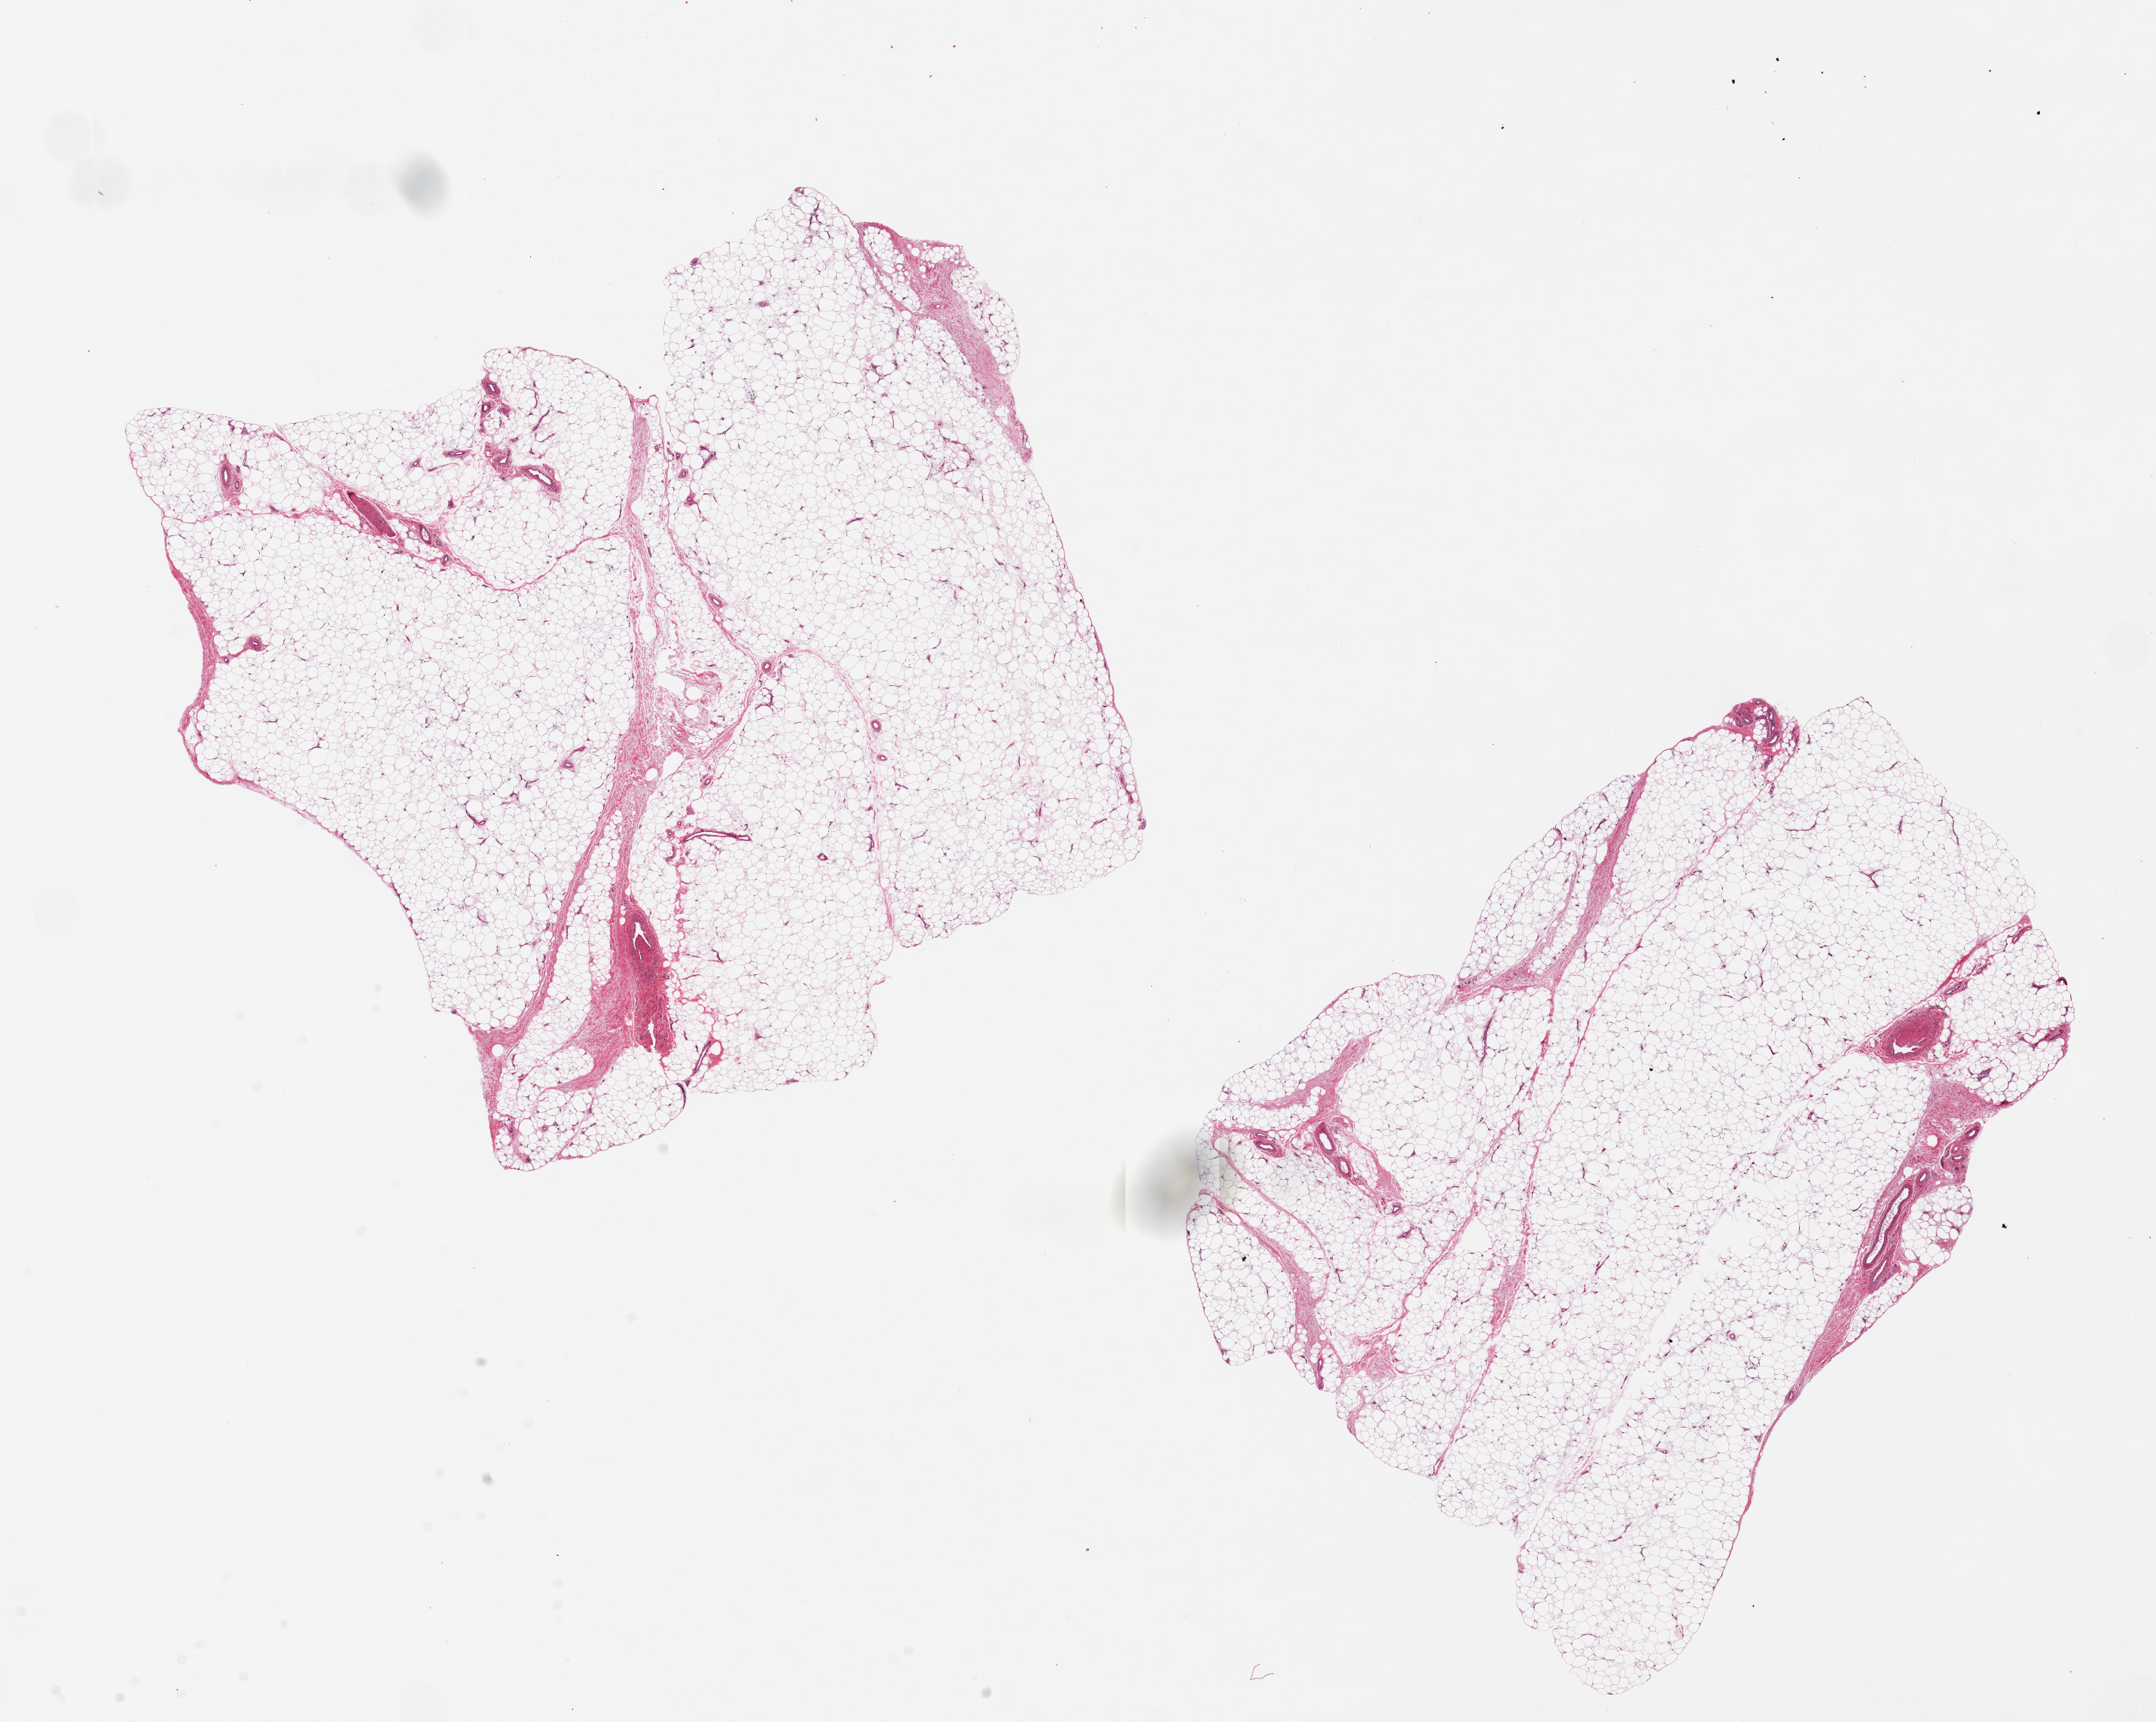
Whole-slide image, hematoxylin and eosin (H&E) stain, brightfield, a low-resolution overview of the entire scanned area, about 22.6 x 18.1 mm (acquisition: 20x scan), PAXgene-fixed paraffin-embedded (PFPE) section, section of adipose tissue (target tissue), tissue donor sample. Male donor.
Reviewer comment on this tissue sample: 2 pieces, 10x9 & 10x8mm.